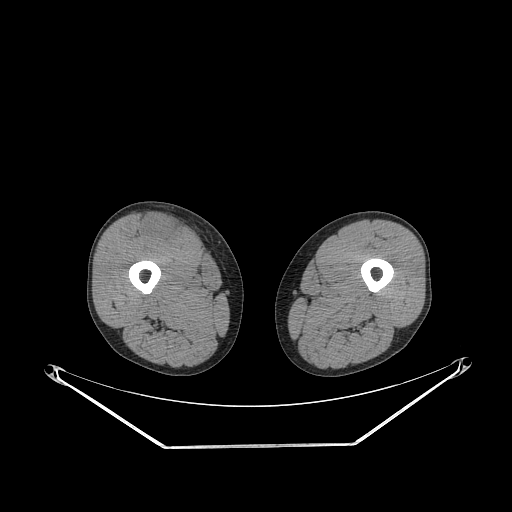
CT of an extremity soft-tissue mass (from a PET/CT study), one axial slice; position 249 of 311 along the scan axis; reconstruction kernel STANDARD; soft-tissue window (W 400 / L 40 HU); 3.75 mm slice thickness; 512 × 512 image matrix, field of view 500 × 500 mm. Male patient. From the clinical record (not read from this slice): histological type: pleiomorphic leiomyosarcoma; grade: intermediate; site of the primary tumour: right thigh.
Outlined on this slice (expert contour drawn on MRI and transferred to this co-registered scan by the dataset authors):
- gross tumour volume including surrounding oedema: box from (x=142, y=215) to (x=181, y=241) px